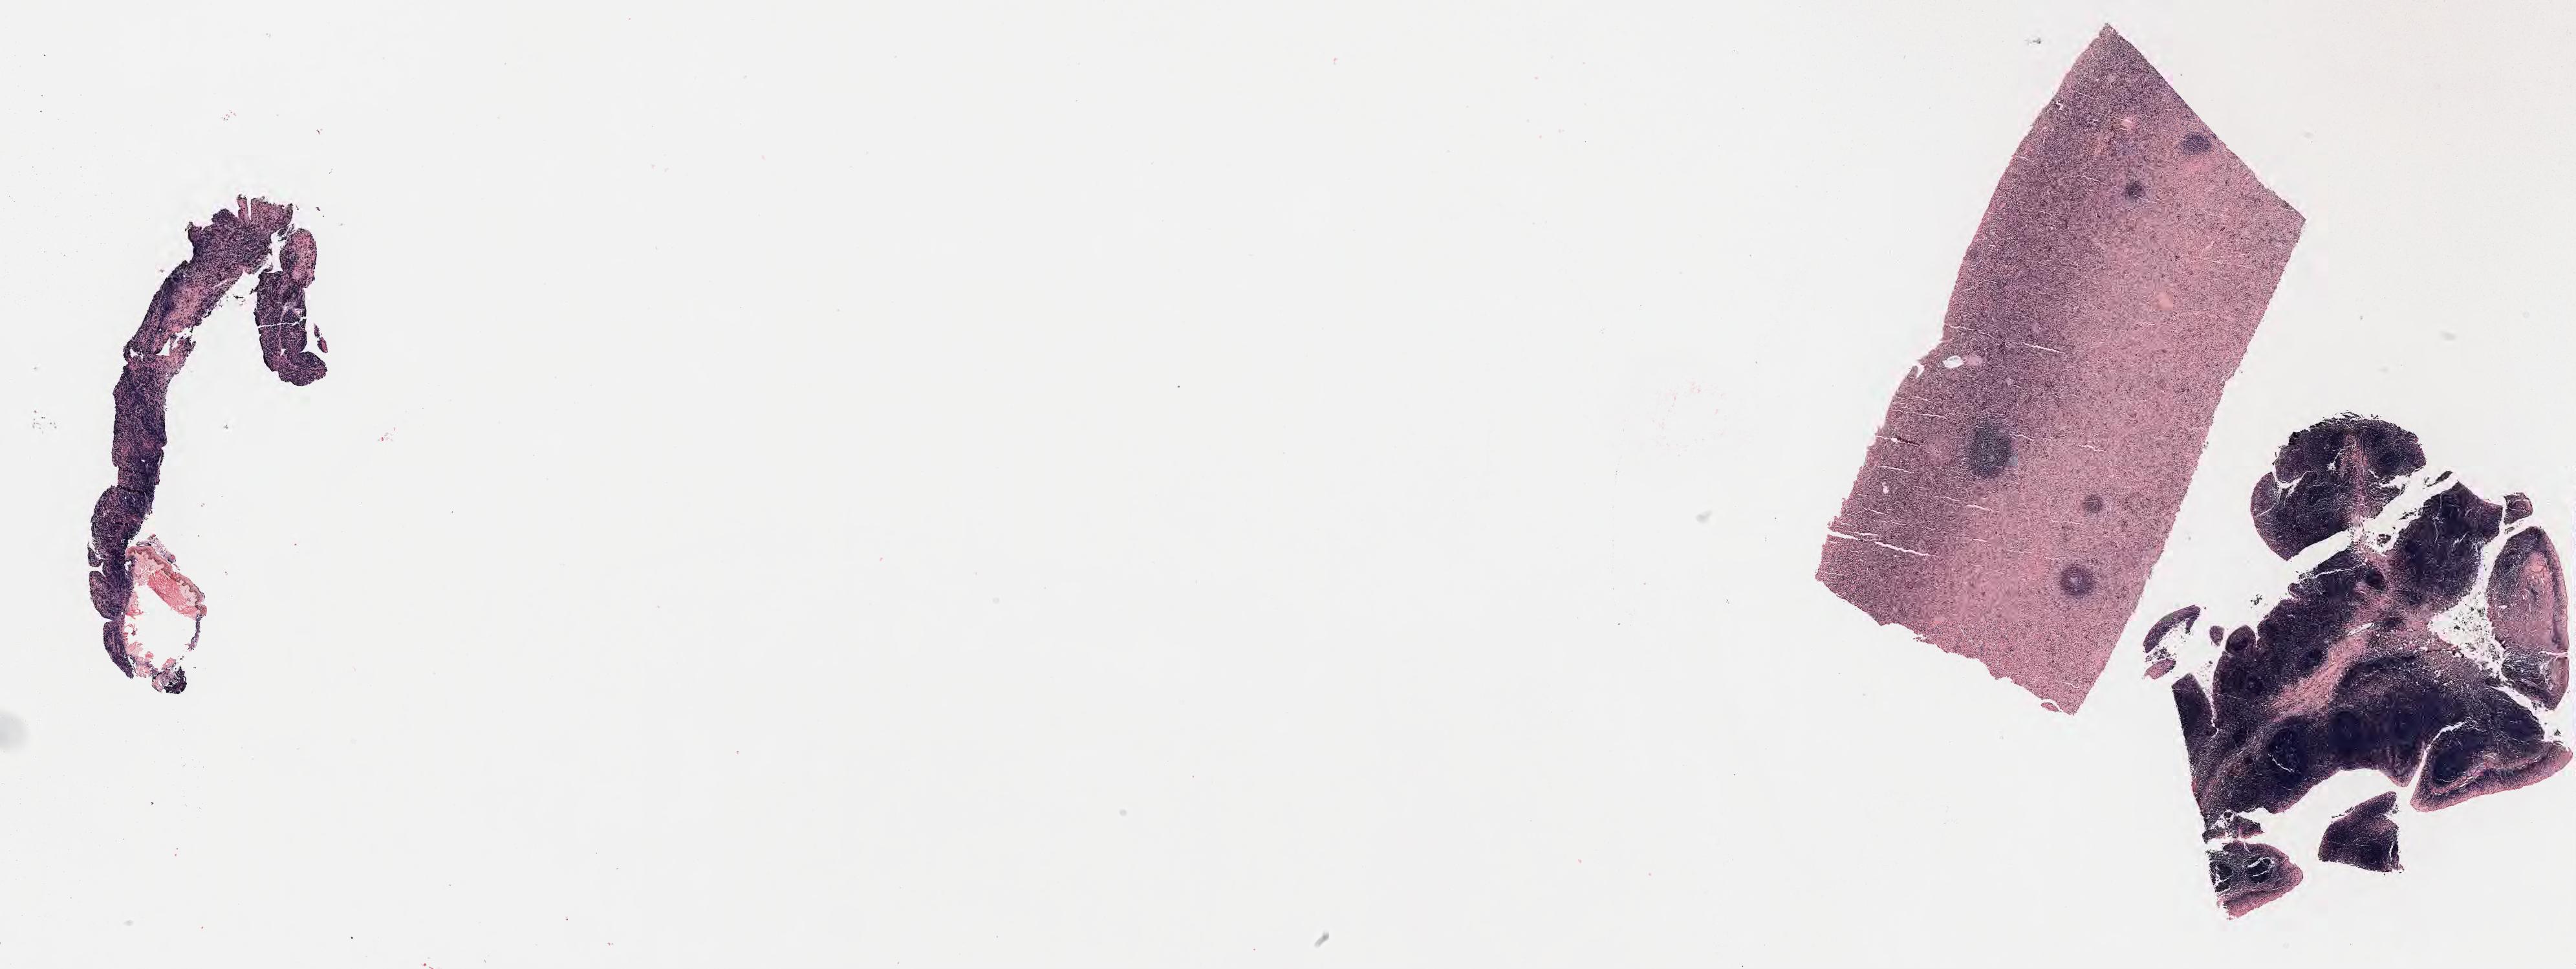
Whole-slide image; stain recorded as Iodonitrotetrazolium — a low-resolution overview of the entire scanned area, about 32.2 x 12.1 mm. Tumor tissue. Patient: female, 43 years old.
• diagnosis: Diffuse large B-cell lymphoma, NOS